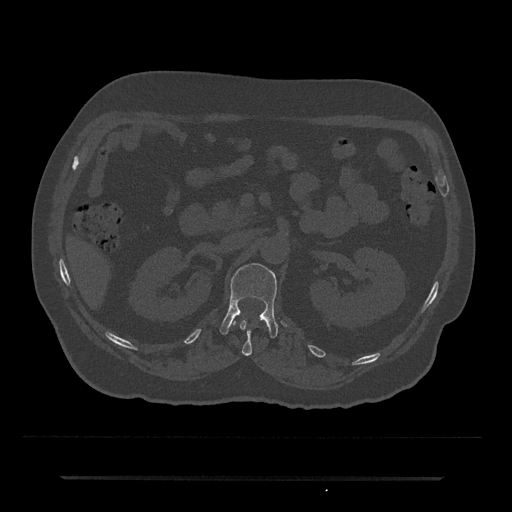
CT including the spine, one axial slice; slice 88 of 797 in the series (ordered by position); reconstruction kernel Br40s/3; 120 kVp; bone window (W 1800 / L 400 HU); 0.5 mm slice thickness; 512 × 512 image matrix, field of view 437 × 437 mm. Patient: male, 69 years. From the clinical record (not read from this slice): primary cancer: prostate.
Annotated regions visible in this slice (semi-automatic segmentation, software-assisted and operator-edited):
- L1 vertebra: box from (x=219, y=263) to (x=278, y=338) px
- T12 vertebra: (x=232, y=317)–(x=267, y=356)